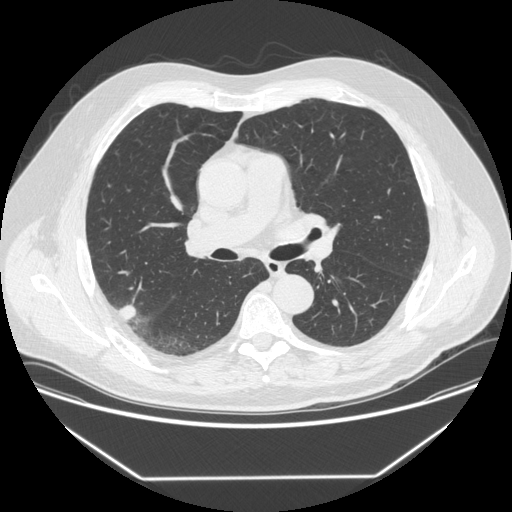
Low-dose screening chest CT, axial slice. First (baseline) screen. Lung window (W 1500 / L -600 HU). 1.25 mm slice thickness. Standard (soft-tissue) reconstruction kernel (STANDARD). 512 × 512 image matrix. Male, age 64 years at enrolment. Former smoker at enrolment.
- Expert-annotated lung lesion, bounding box (x1, y1, x2, y2) in pixels: (102, 299, 144, 332).
- The exam's reader record, not a measurement of the box and not confirmed to be the same lesion: non-calcified nodule or mass ≥4 mm, right upper lobe, 12 × 12 mm, smooth margins, soft tissue attenuation.
- Official screen result: positive, change unspecified: nodule(s) >= 4 mm or enlarging nodule(s), mass(es), or other non-specific abnormalities suspicious for lung cancer.
- Later outcome: lung cancer diagnosed 92 days after this screen — adenocarcinoma, NOS, right upper lobe, poorly differentiated (G3), stage IIIB (AJCC 6th edition), 15 mm at pathology.